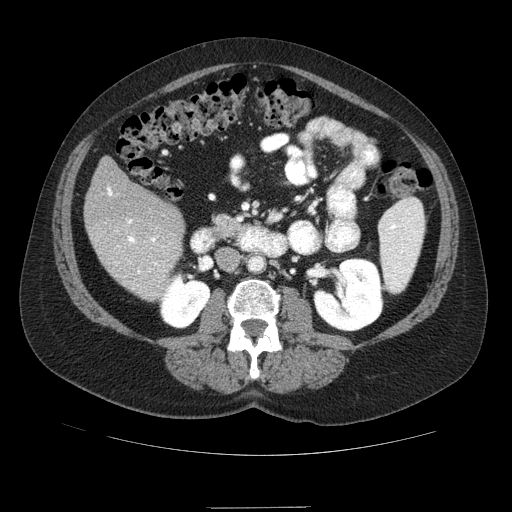
Contrast-enhanced abdominal CT (liver protocol), one axial slice. Slice 26 of 89 in the series (ordered by position). Reconstruction kernel STANDARD. Soft-tissue window (W 400 / L 40 HU). 2.5 mm slice thickness. 512 × 512 image matrix. From the clinical record (not read from this slice): diagnosis: hepatocellular carcinoma (patient treated with transarterial chemoembolisation; whether this scan precedes or follows treatment is not stated here); TNM stage (as recorded): Stage-IIIB; Child-Pugh class: A; tumour nodularity: multinodular.
Outlined on this slice (semi-automatically segmented with operator editing):
- liver parenchyma outside the tumour (the mass and vessels are separate outlines, so this box may not span the whole liver): bounding box <84,156,184,300> (left, top, right, bottom; pixels)
- liver vessels: <107,187,157,273>